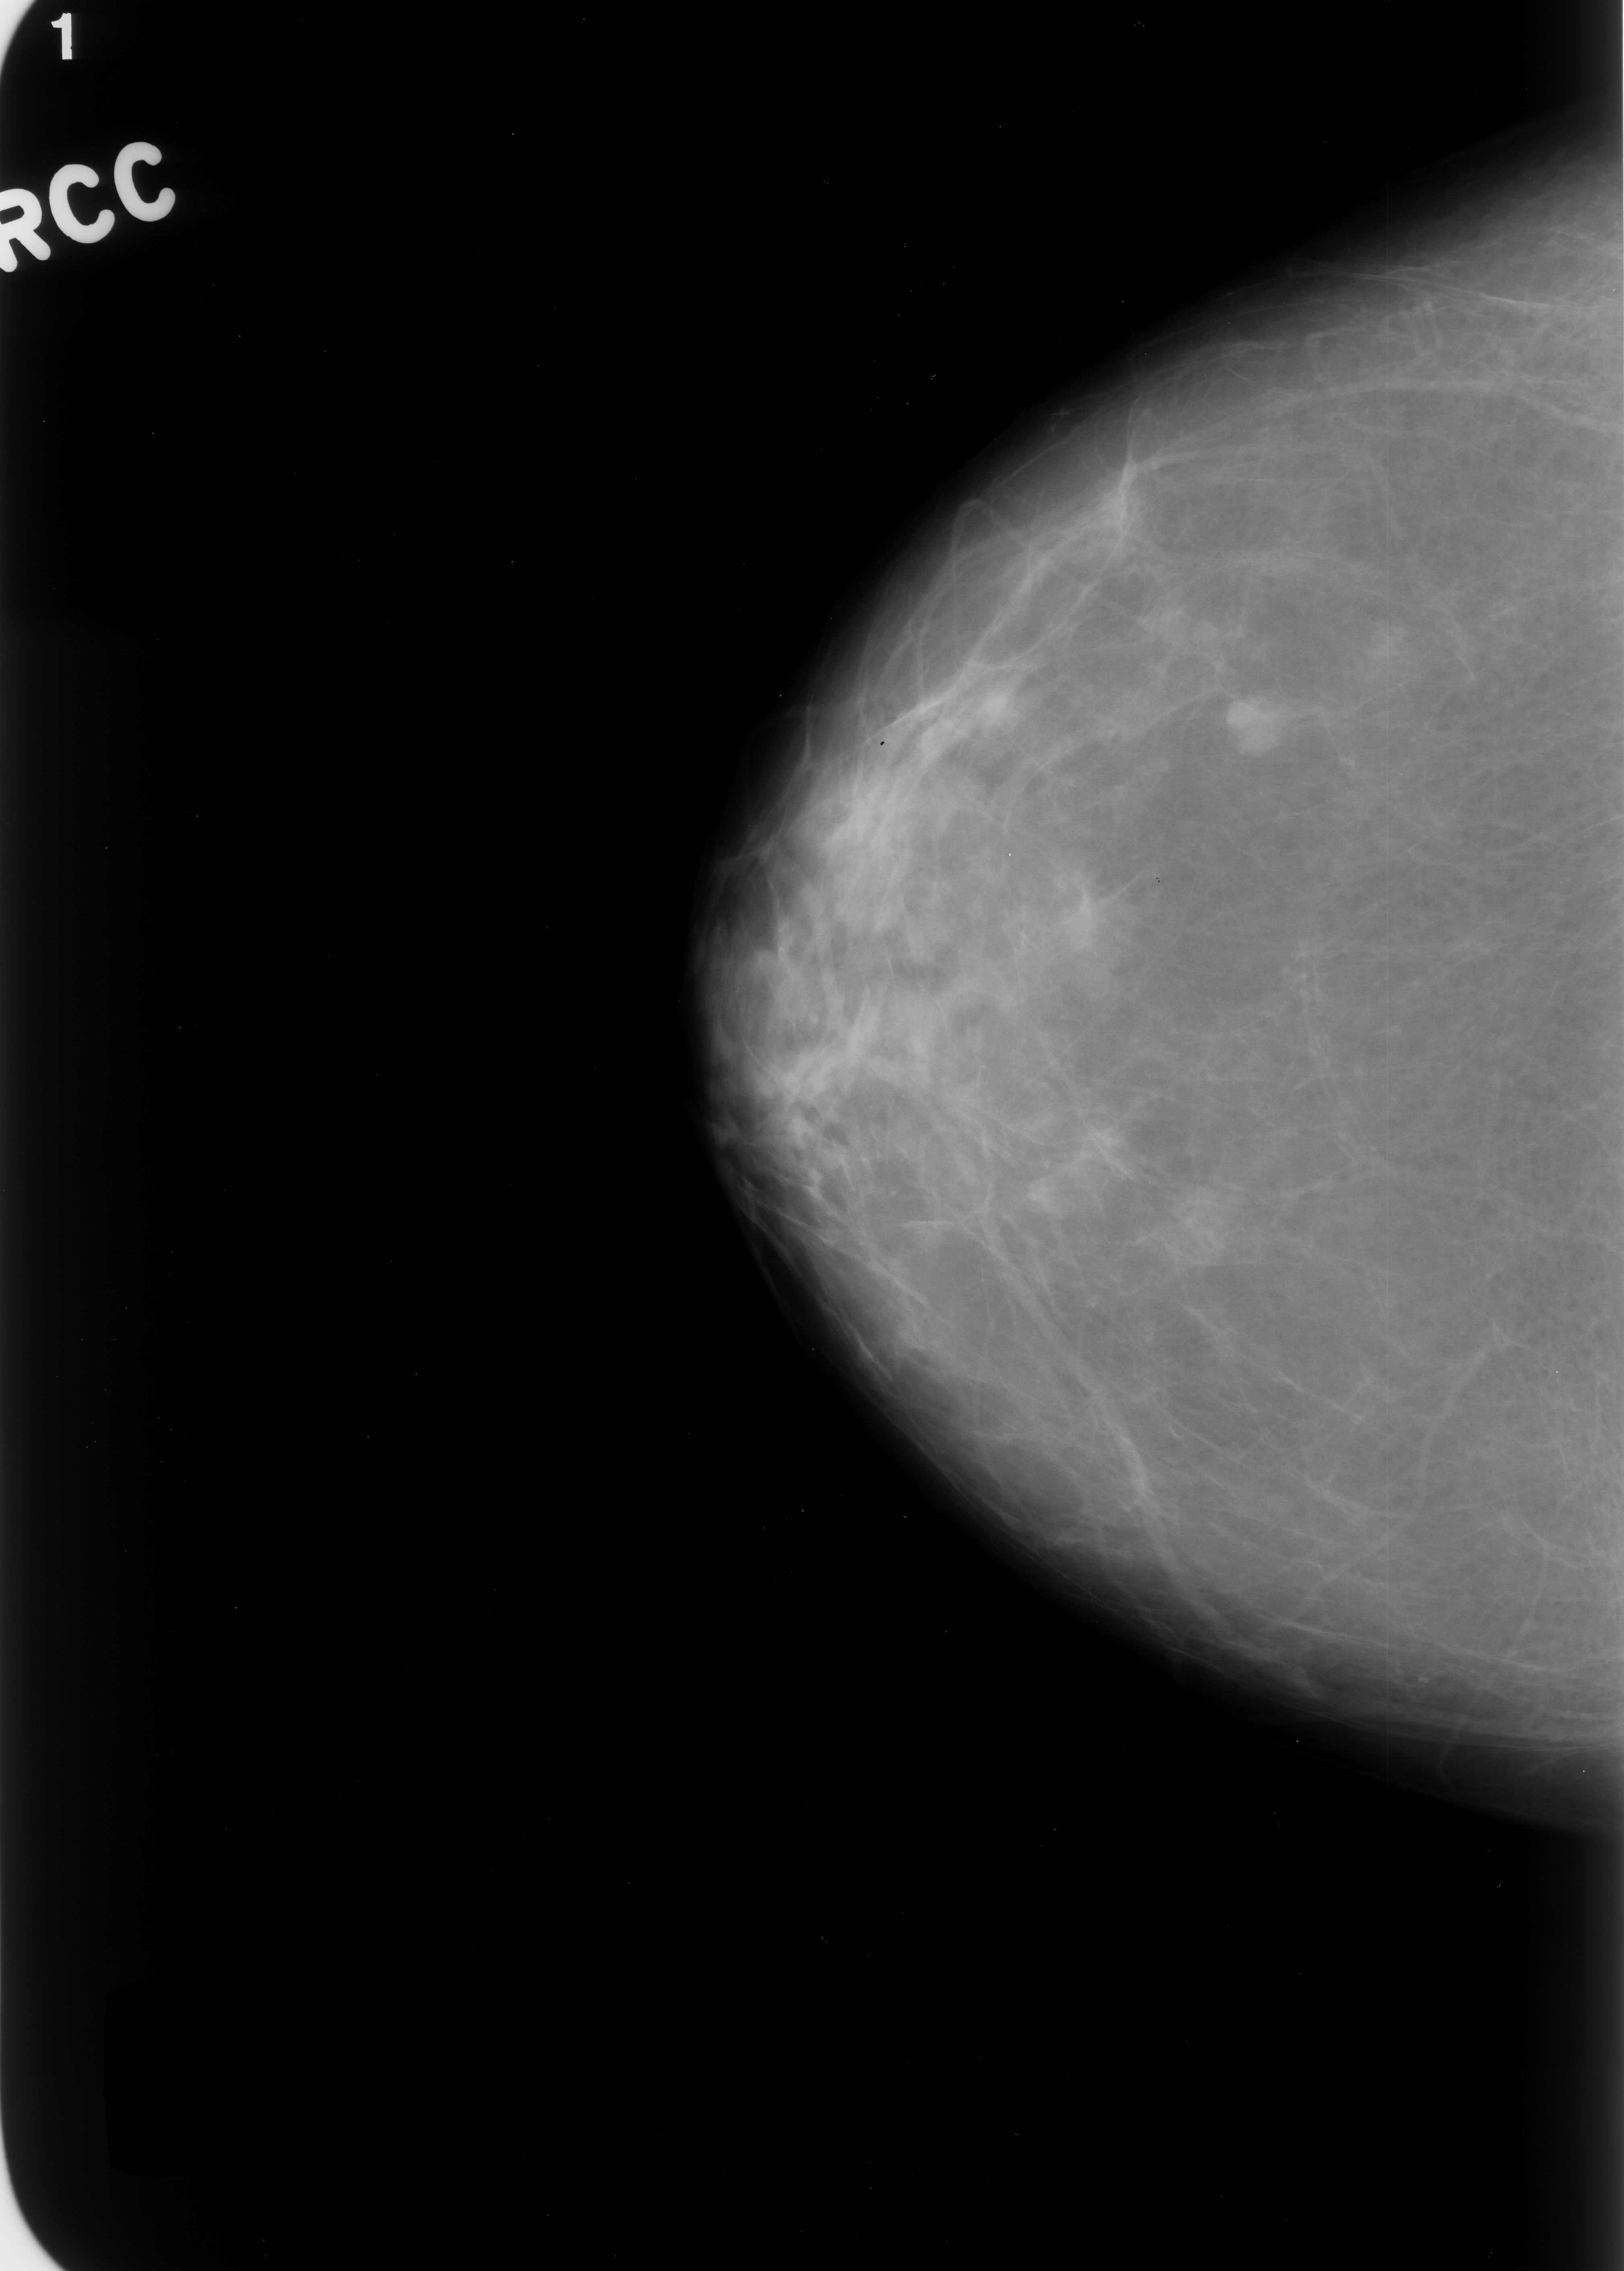
Digitized screen-film mammogram; right breast; craniocaudal (CC) view; BI-RADS breast density category 2 (scale 1–4); 1624 × 2271 image matrix.
Expert-marked regions of interest on this film, with their recorded descriptors:
- mass, shape lobulated, margins circumscribed; BI-RADS assessment category 2; subtlety rating 5 on a 1 (subtle) to 5 (obvious) scale; outcome (as recorded, no biopsy): benign without callback (not worked up further): bounding box (x1, y1, x2, y2) in pixels: (1207, 678, 1316, 762)